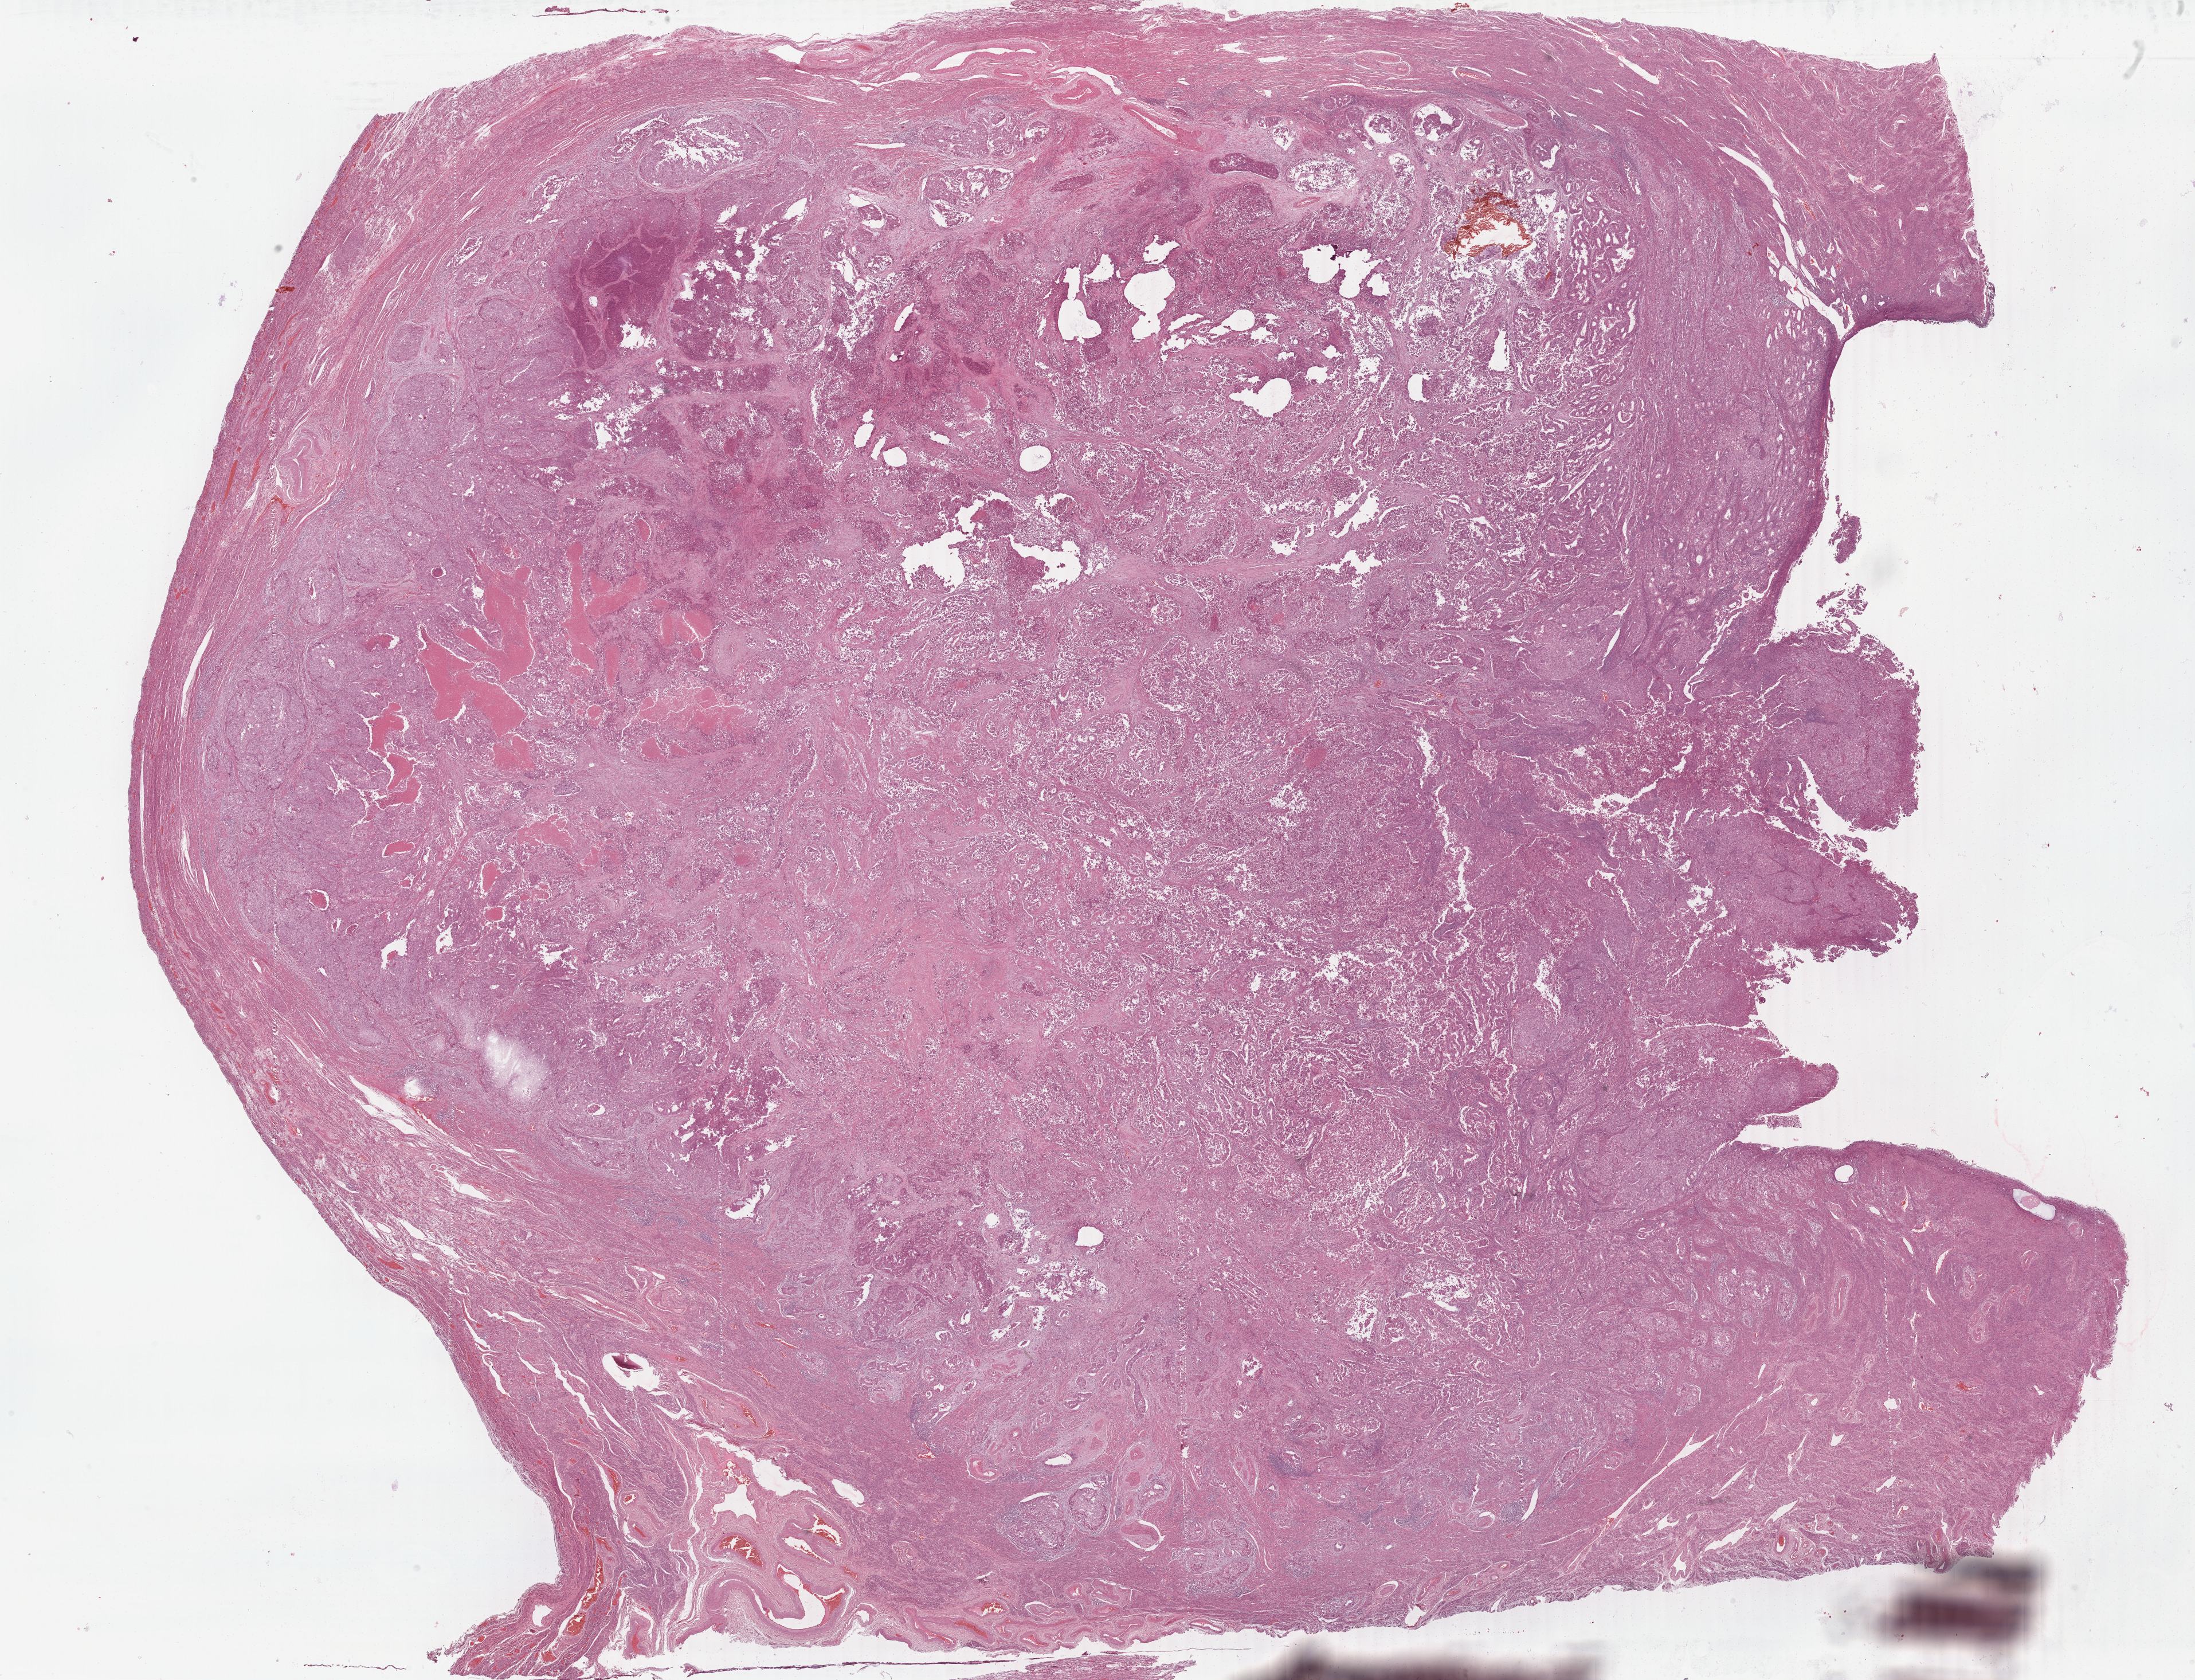
H&E-stained whole-slide image — whole scanned area (about 30.5 x 23.3 mm, from a 40x scan) shown as a low-resolution overview, formalin-fixed paraffin-embedded (FFPE) diagnostic section, primary tumour sample from the uterus. Patient: female, age at initial diagnosis 64 years.
Histologic diagnosis: Endometrioid adenocarcinoma, NOS.